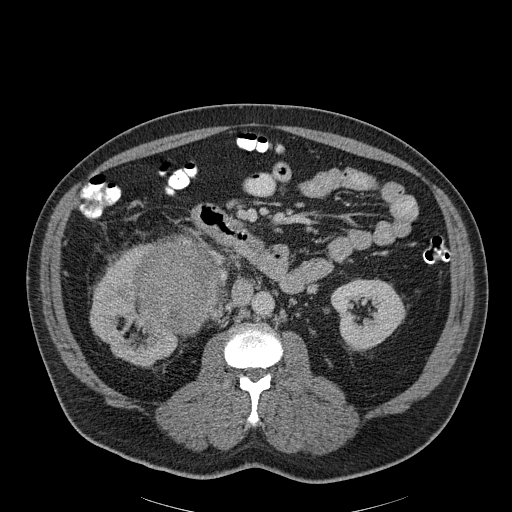
Contrast-enhanced abdominal CT, one axial slice. Slice 107 of 186 in the series (ordered by position). Soft-tissue window (W 400 / L 40 HU). 512 × 512 image matrix. Male patient, age 56 years. From the clinical record (not read from this slice): diagnosis: adrenocortical carcinoma; tumour side: right adrenal; tumour size at pathology: 18 cm; Ki-67 index: 2 %; stage (as recorded): 3.
Annotated regions visible in this slice (semi-automatically segmented with operator editing):
- mass: bounding box (x1, y1, x2, y2) in pixels: (139, 239, 218, 335)